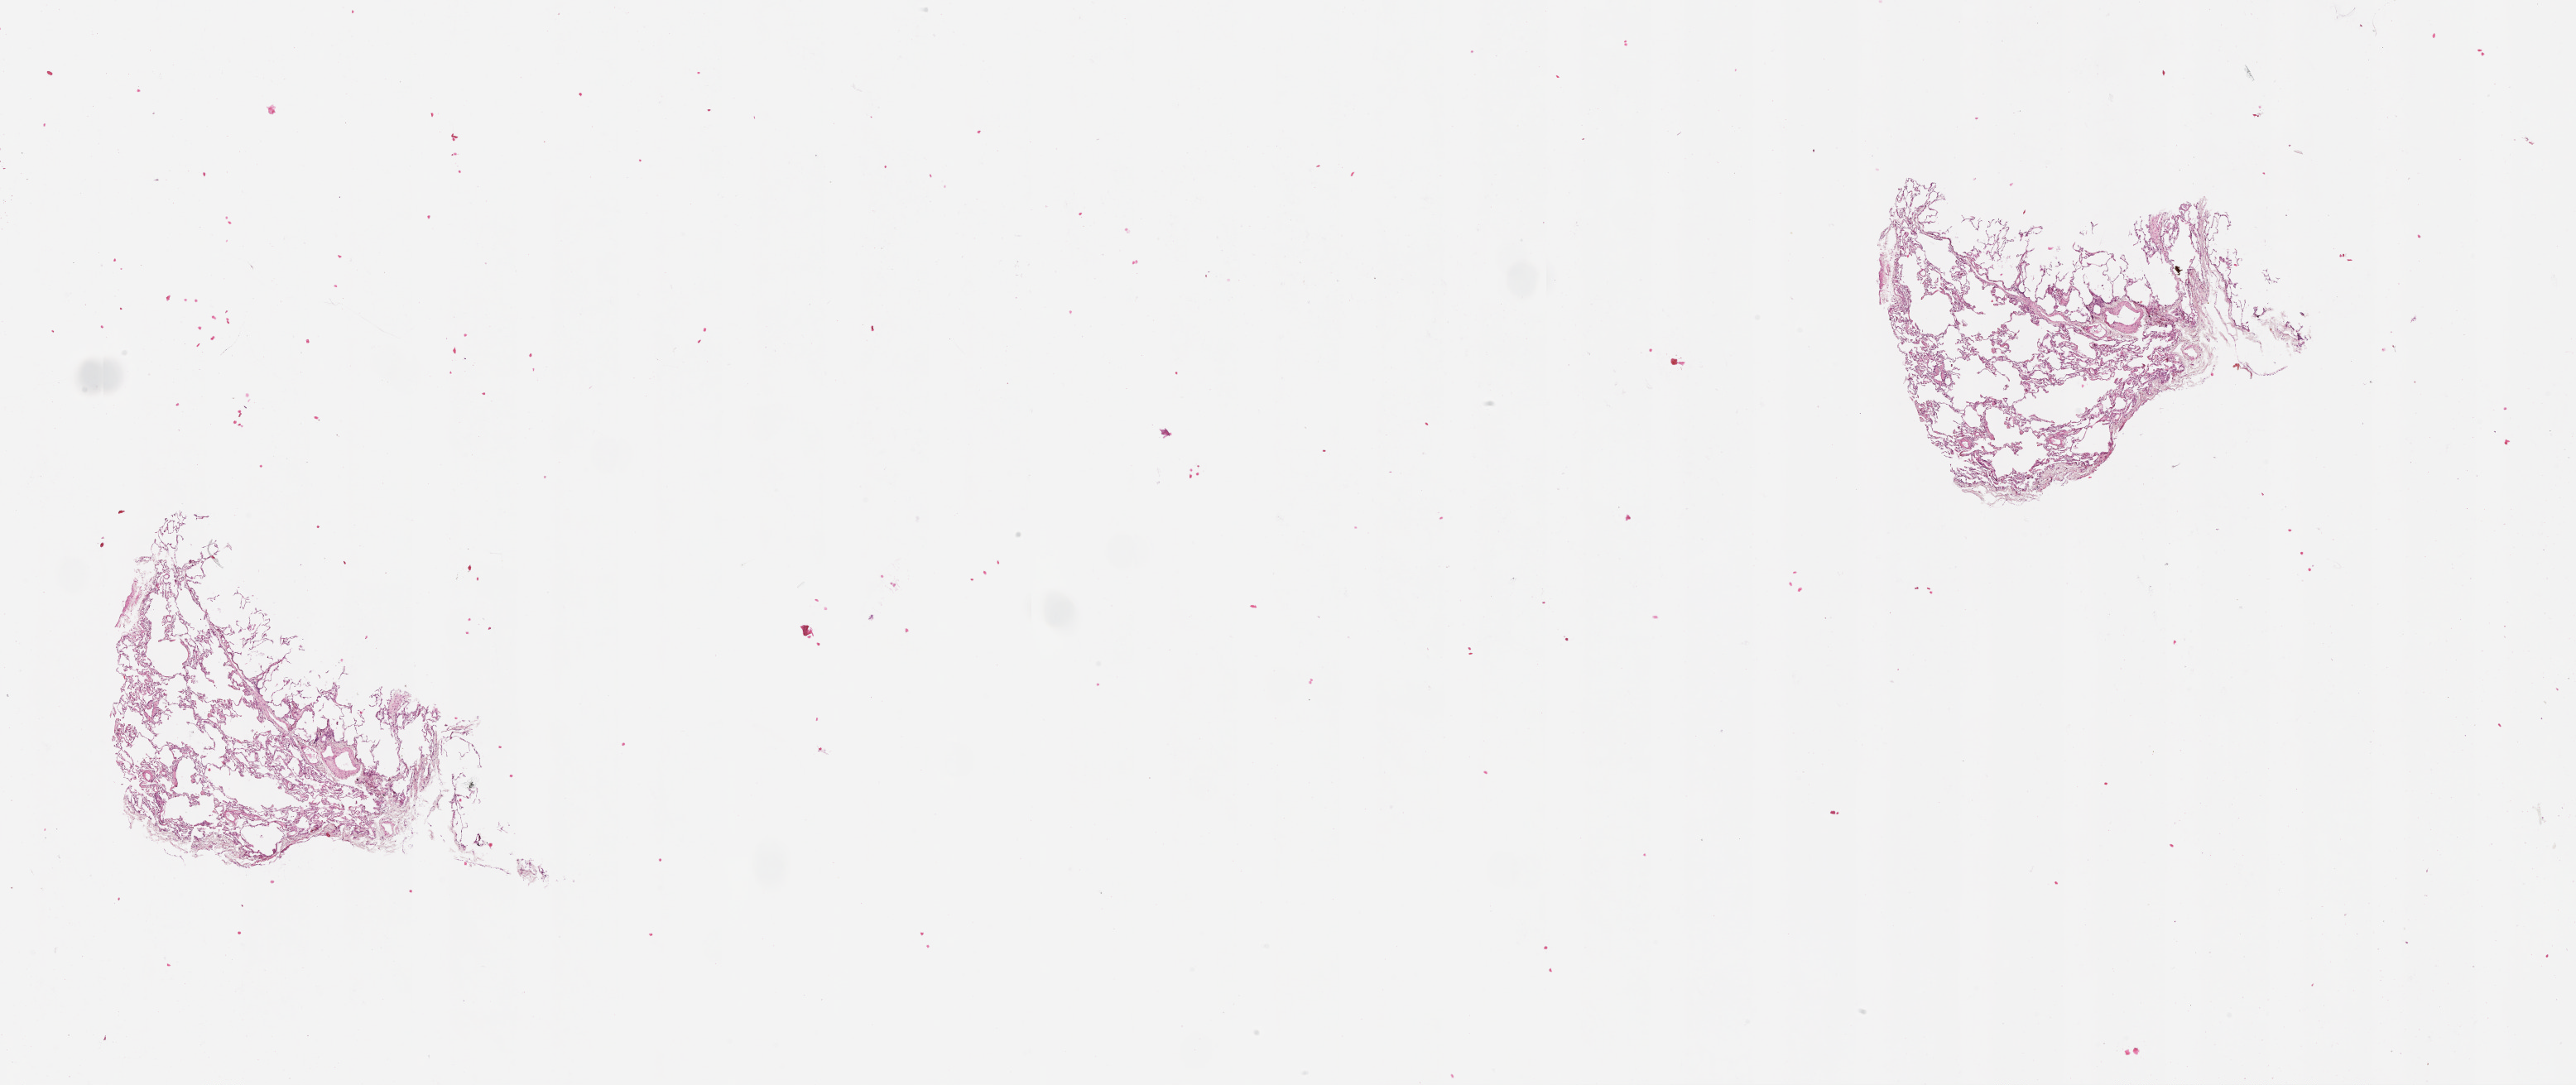
H&E-stained whole-slide image — whole scanned area (about 25.1 x 10.6 mm, acquisition: 20x scan) shown as a low-resolution overview; normal (non-tumour) tissue sample, lung. 61-year-old male patient.
This section: normal (non-tumour) tissue from the same patient. Patient diagnosis (cohort enrolment): squamous cell carcinoma (lung).